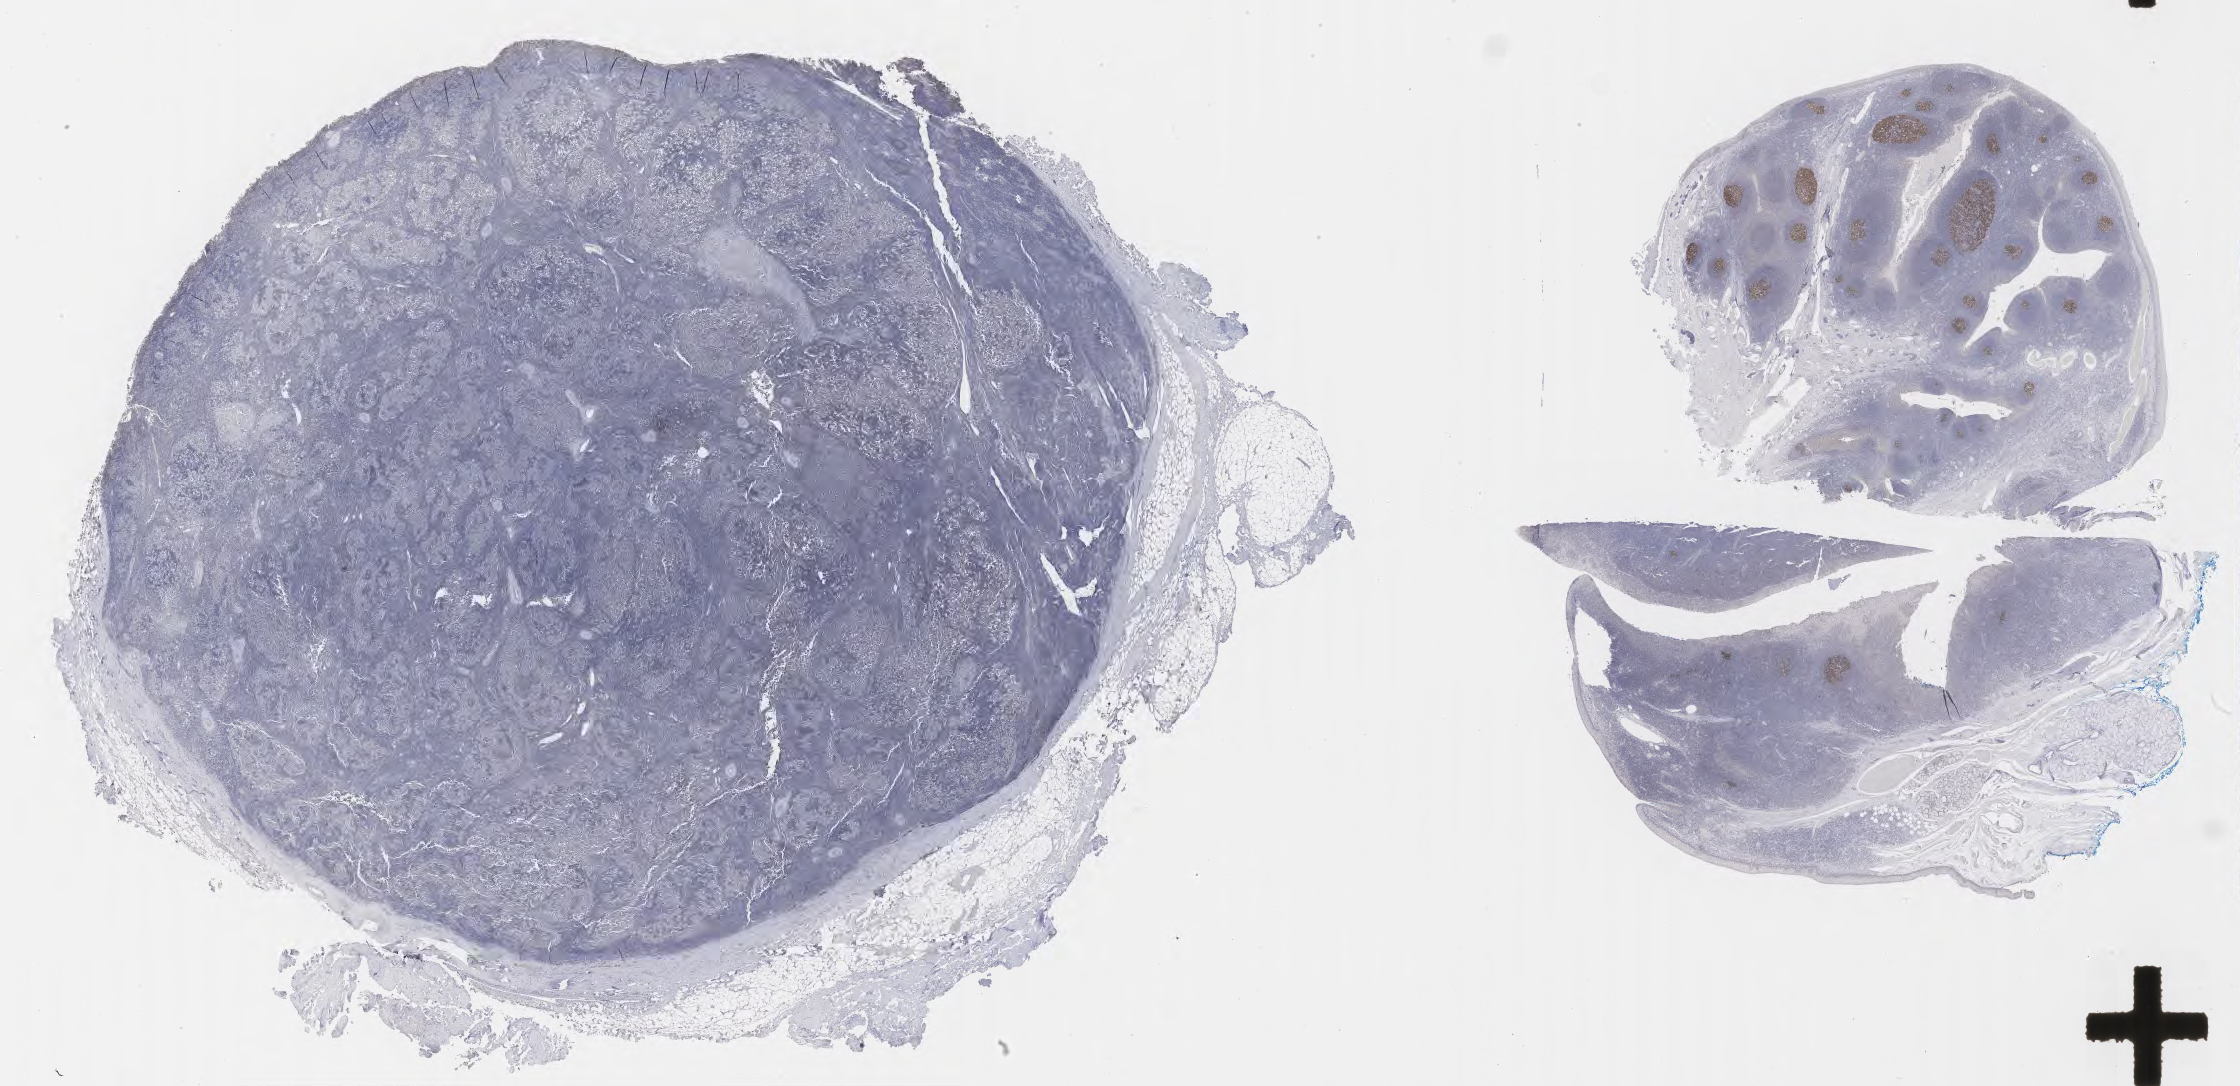
Whole-slide image, immunohistochemical stain for BCL6, whole scanned area (about 36.2 x 17.6 mm) shown as a low-resolution overview, tumor tissue, anatomic site: lymph node. Male patient, age 46 years.
Histologic diagnosis: Diffuse large B-cell lymphoma, NOS.